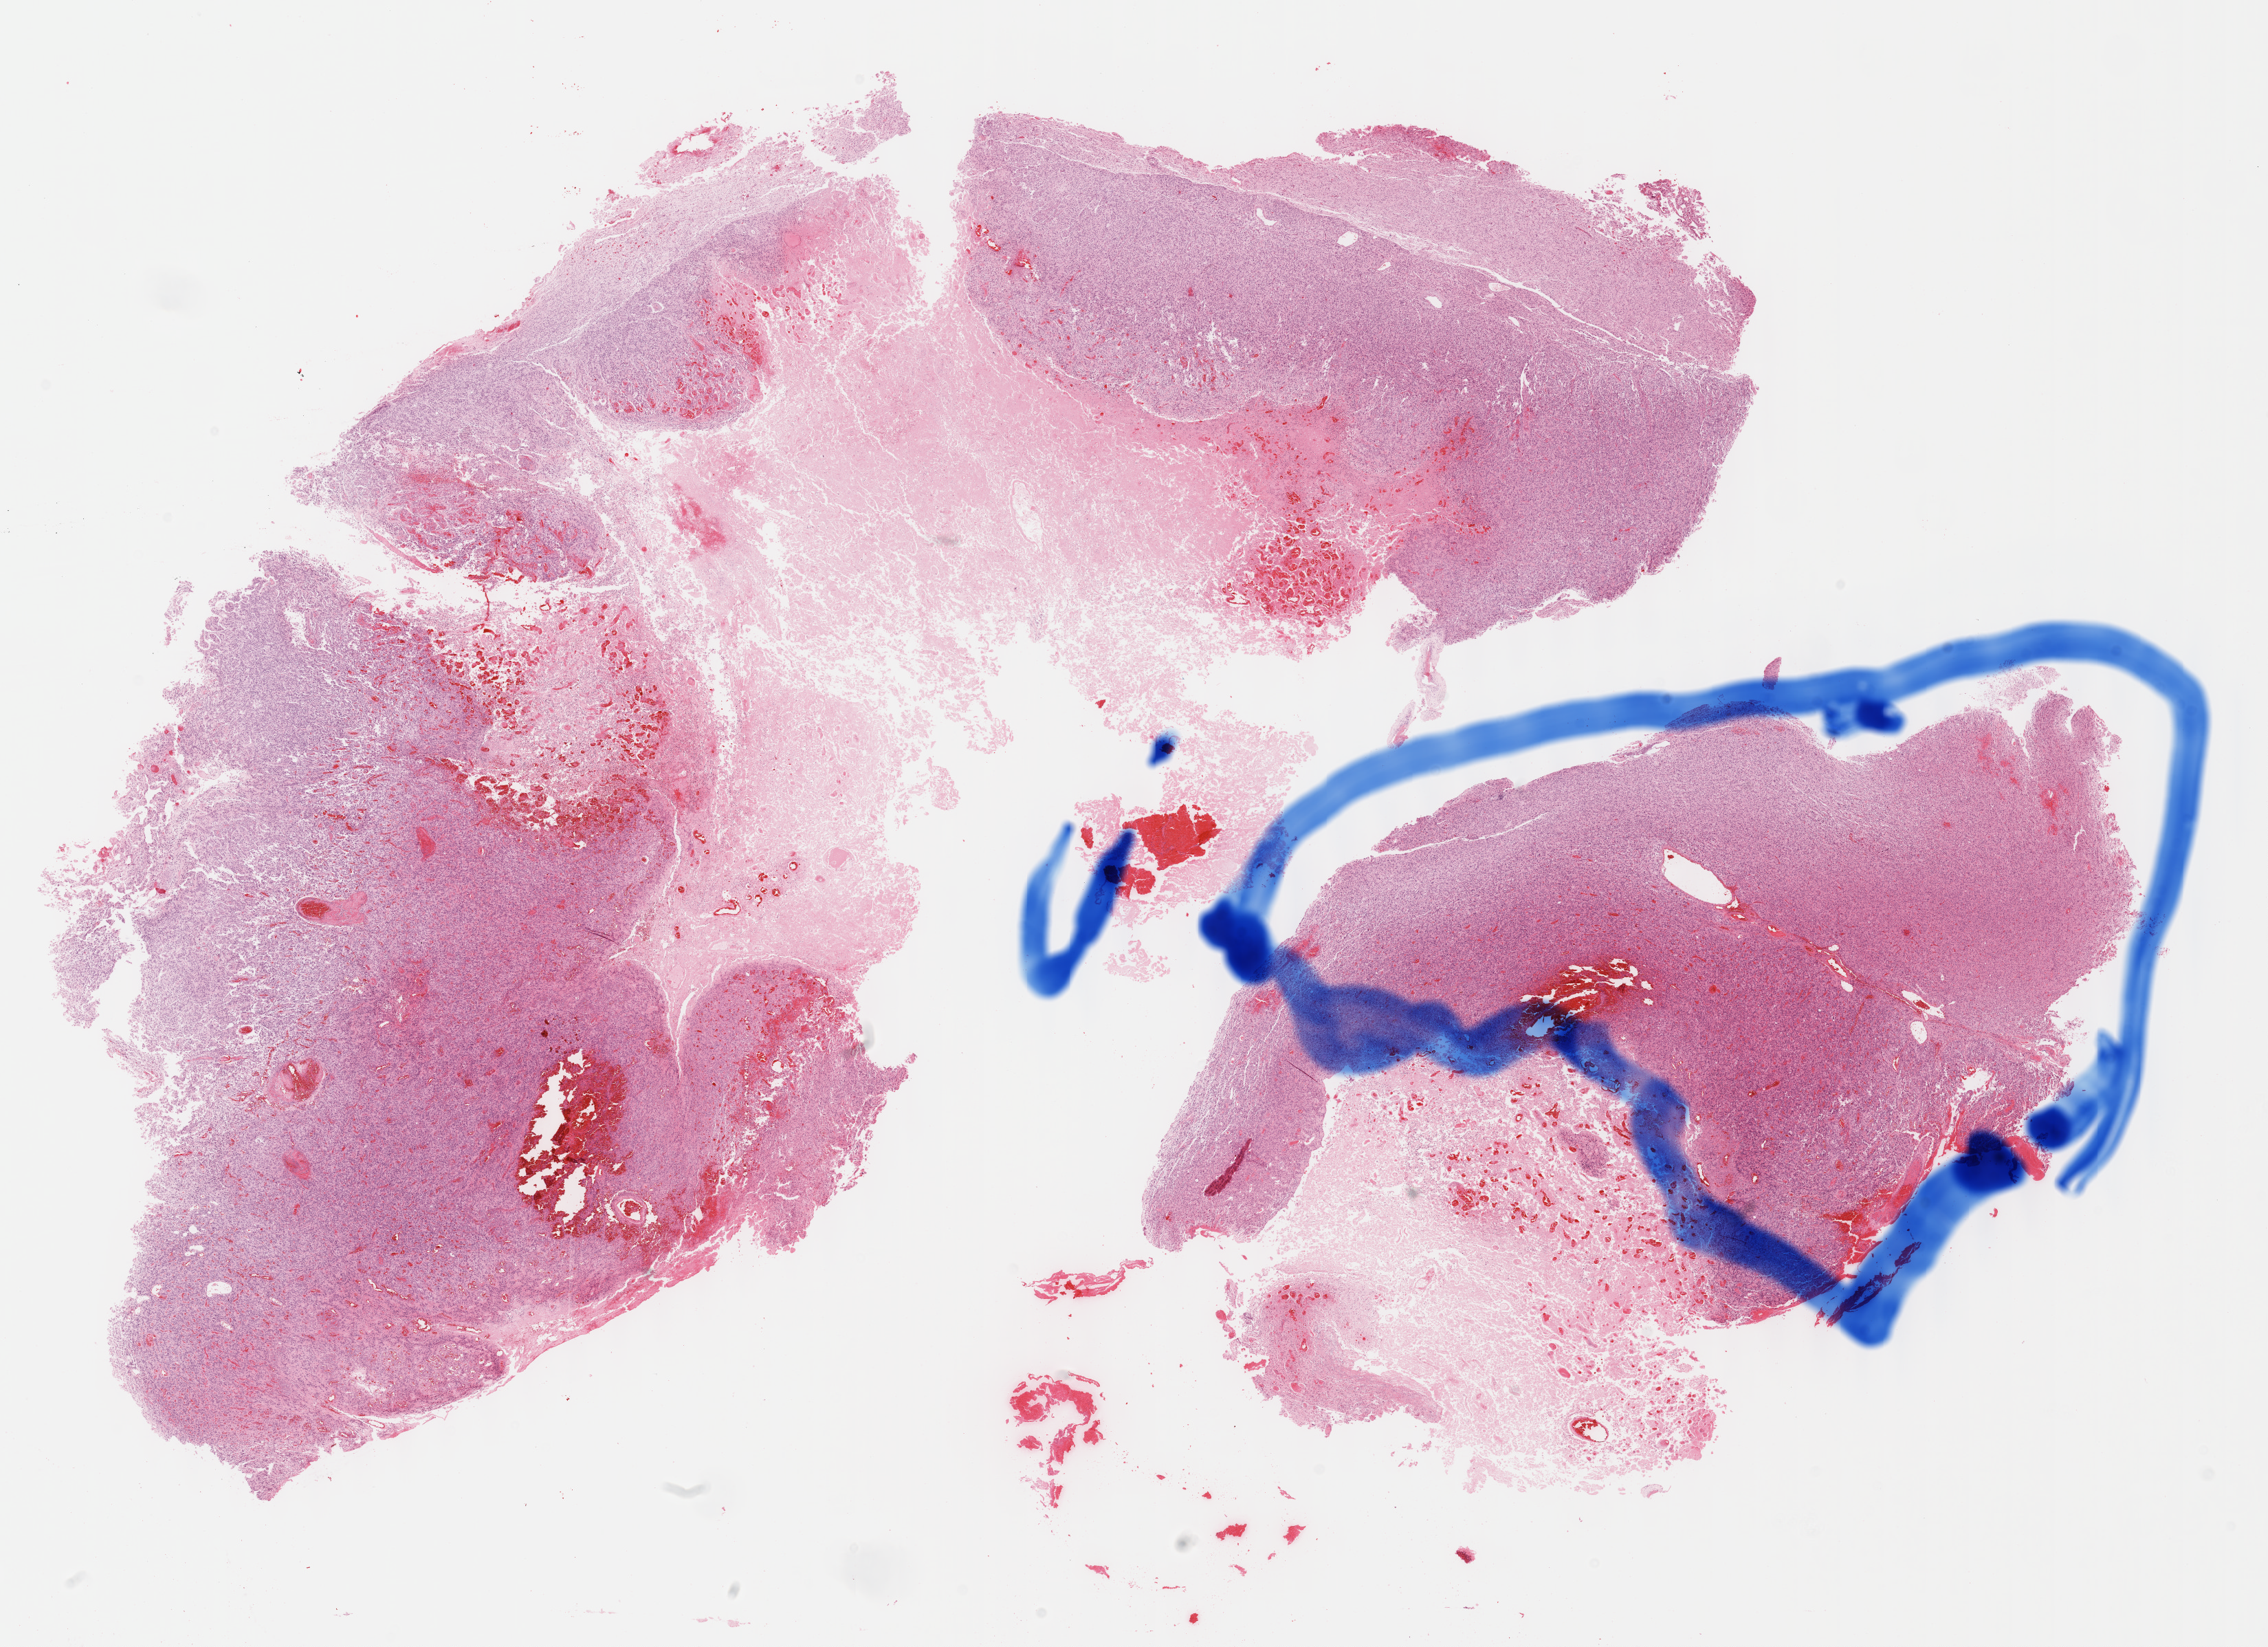
Digitized H&E tissue section (whole slide) — a low-resolution overview of the entire scanned area, about 26.7 x 19.4 mm (acquisition: 40x scan); formalin-fixed paraffin-embedded (FFPE) diagnostic section; sample: primary tumour, brain. Female patient; age at initial diagnosis 69 years.
* diagnosis: Glioblastoma